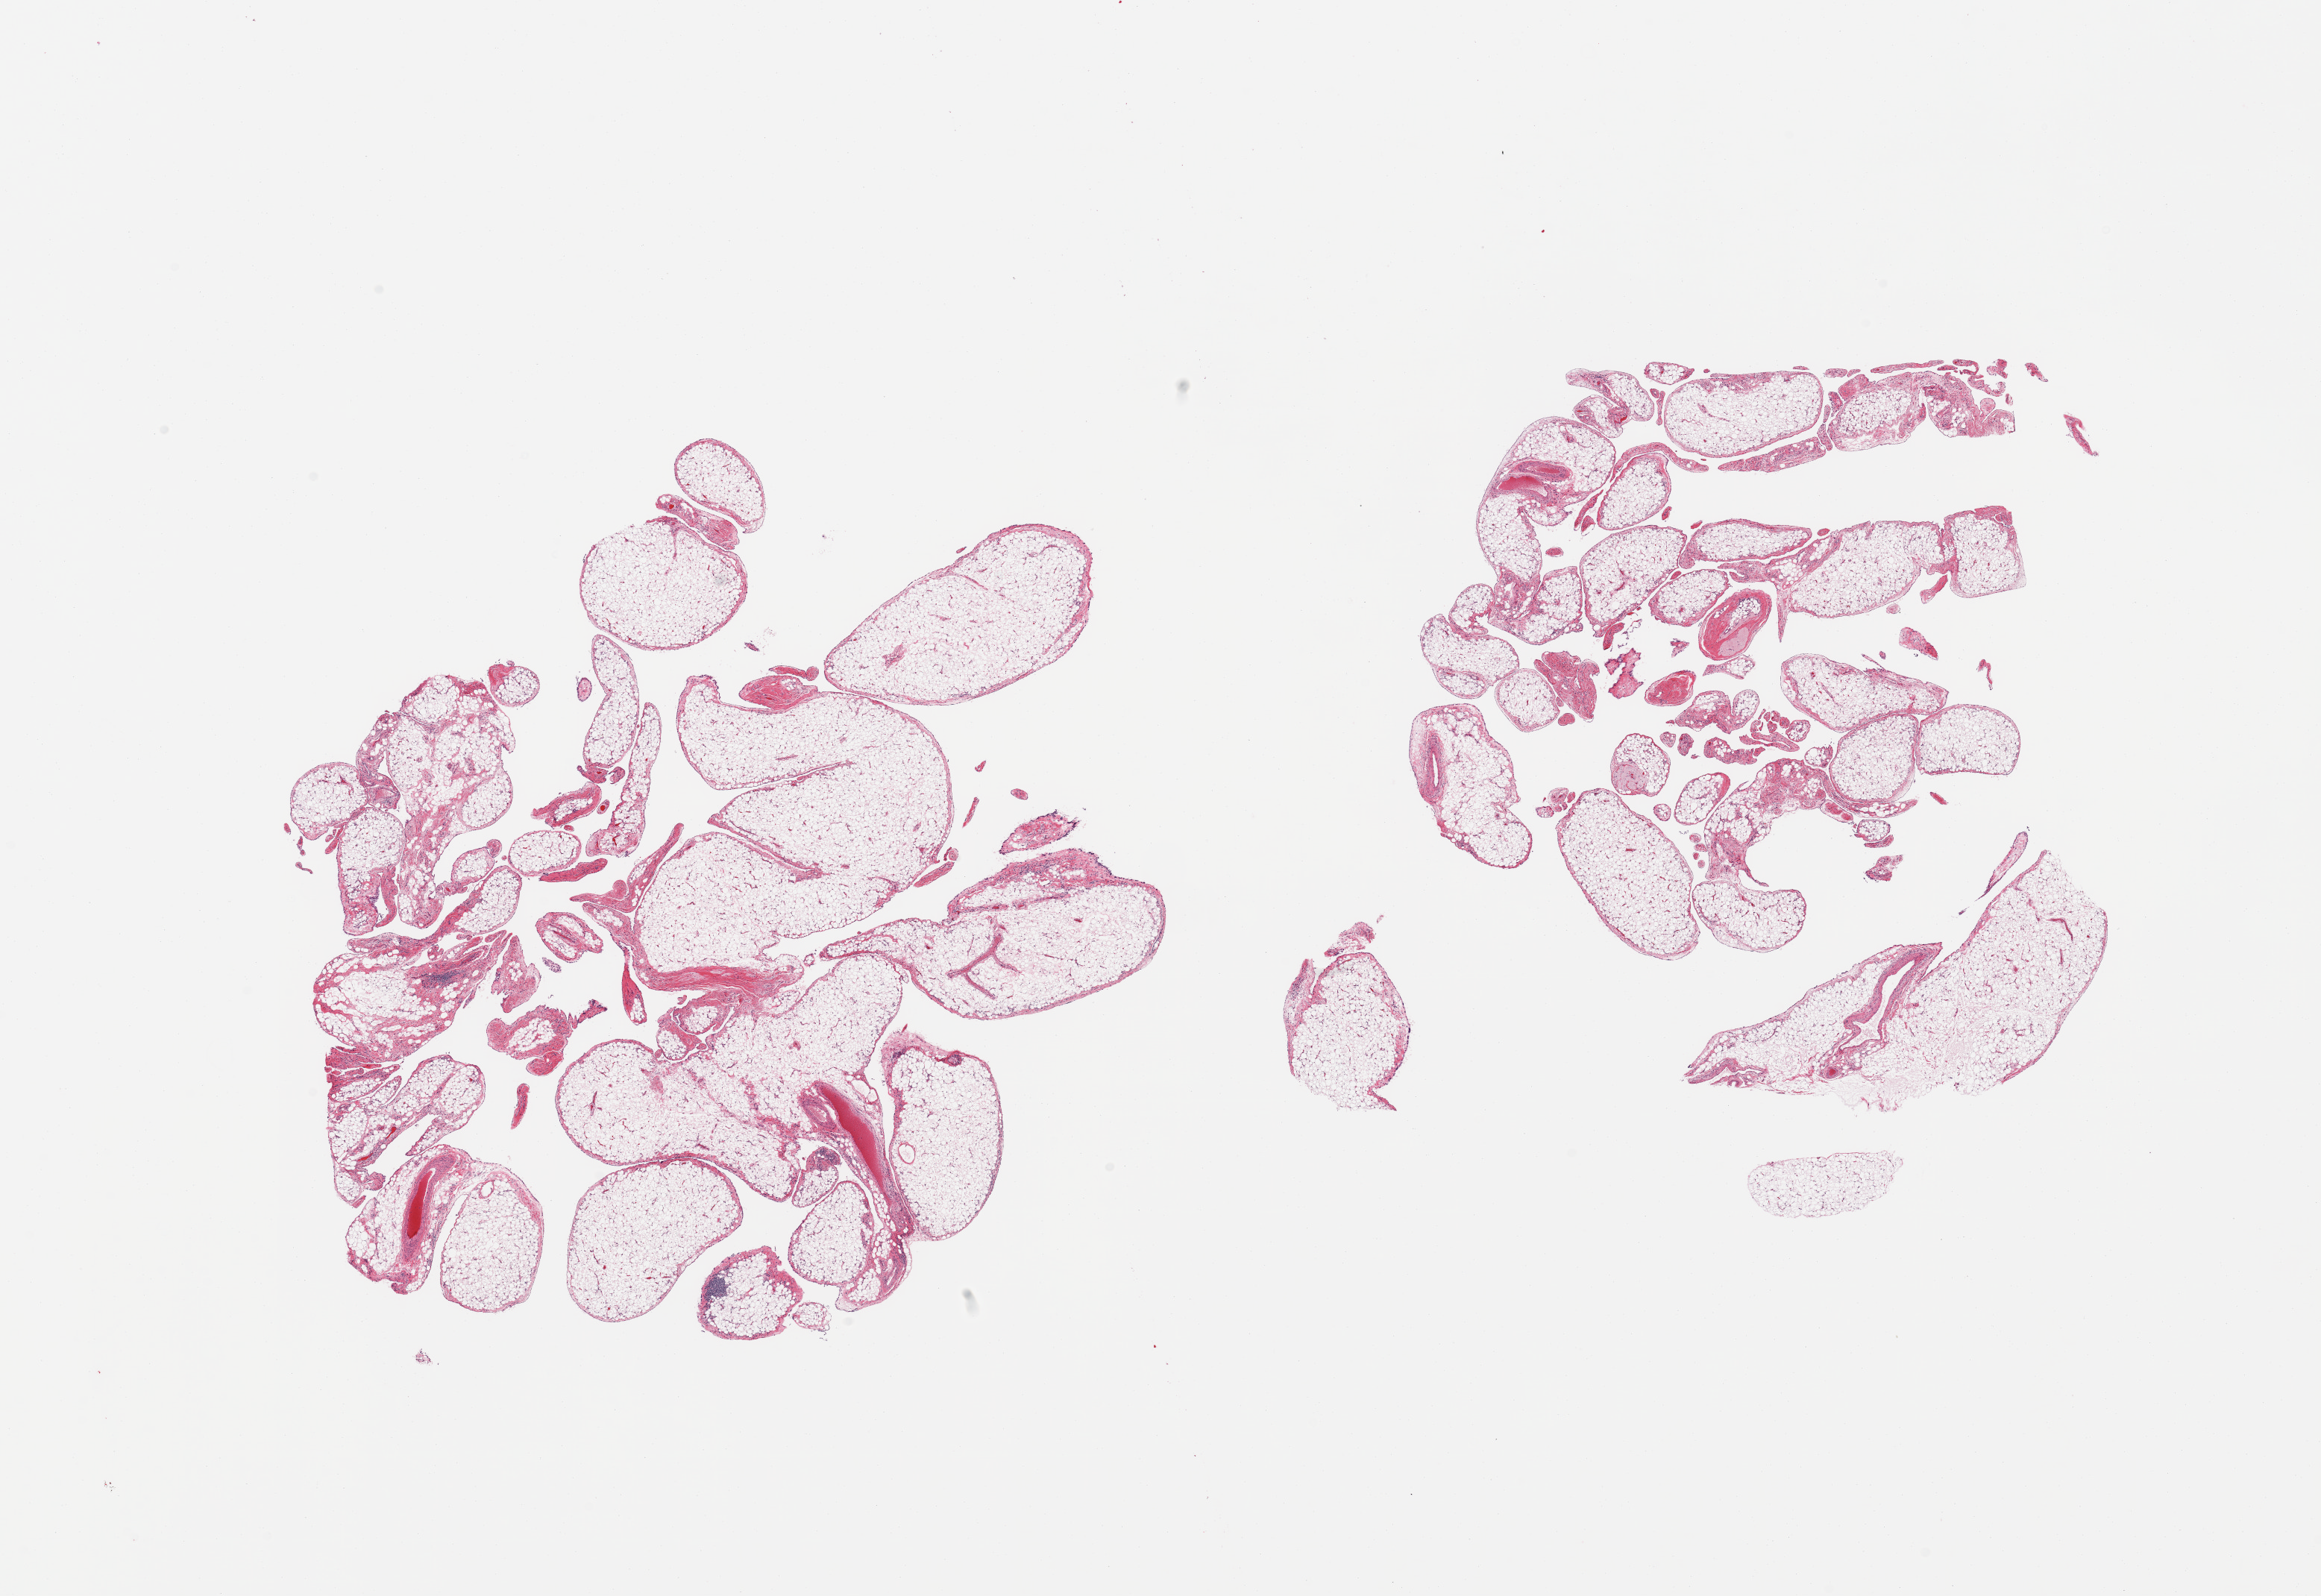
Haematoxylin and eosin whole-slide image, brightfield — whole scanned area (about 24.6 x 16.9 mm) shown as a low-resolution overview; PAXgene-fixed paraffin-embedded (PFPE) section; section of omentum (target tissue); tissue donor sample. Male donor.
Reviewer comment on this tissue sample: 2 pieces; multilobulated; 5% fibrous content.